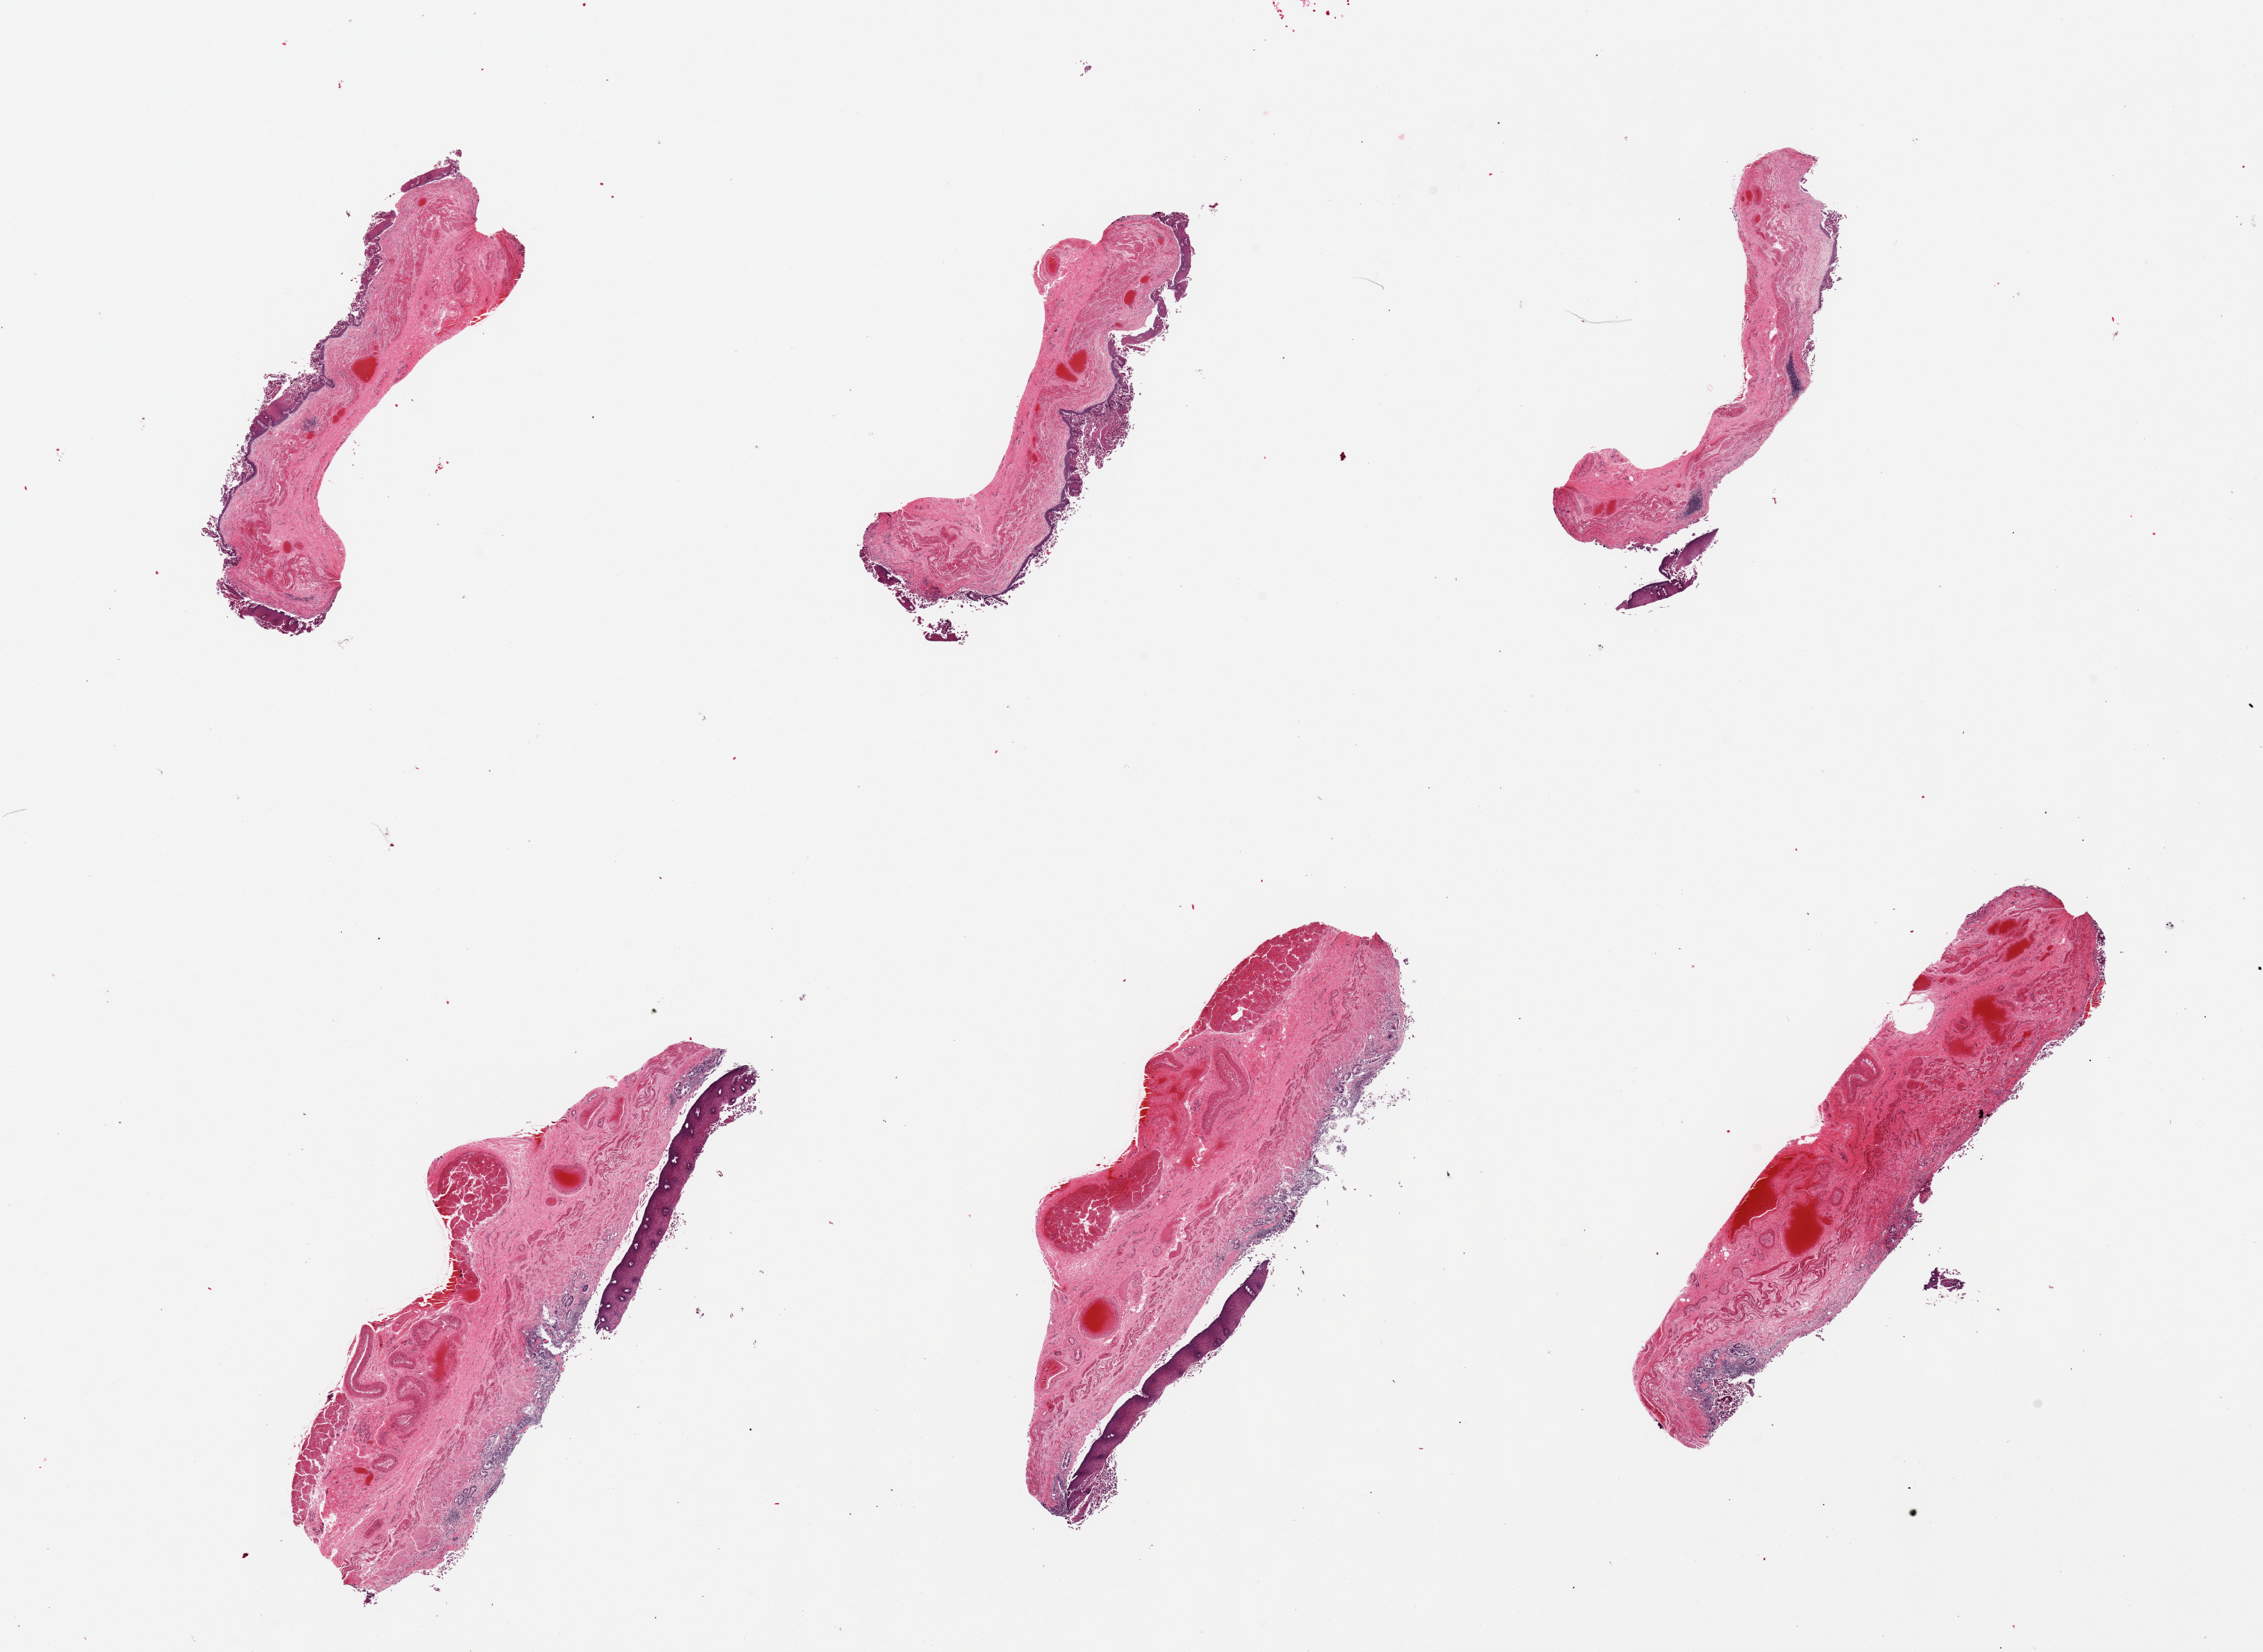
H&E whole-slide image, brightfield, low-resolution overview of the scanned area, about 25.6 x 18.7 mm, PAXgene-fixed, paraffin-embedded tissue, target tissue: esophageal mucous membrane, donor tissue sample. Donor: male.
Reviewer comment on this tissue sample: 6 pieces; fragmented squamocolumnar mucosa with chronic inflammation and goblet cells consistent with peptic reflux and Barrett esophagus.